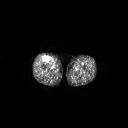
FDG PET of an extremity soft-tissue mass (from a PET/CT study), one axial slice. Slice 256 of 311 in the series (ordered by position). 3.27 mm slice thickness. 128 × 128 image matrix, field of view 700 × 700 mm. Patient: male, 56 years. Case-level facts recorded for this patient, not image findings: histological type: pleiomorphic leiomyosarcoma; grade: intermediate; site of the primary tumour: right thigh.
Annotated regions visible in this slice (expert contour drawn on MRI and transferred to this co-registered scan by the dataset authors):
- gross tumour volume including surrounding oedema: box from (x=42, y=56) to (x=51, y=62) px